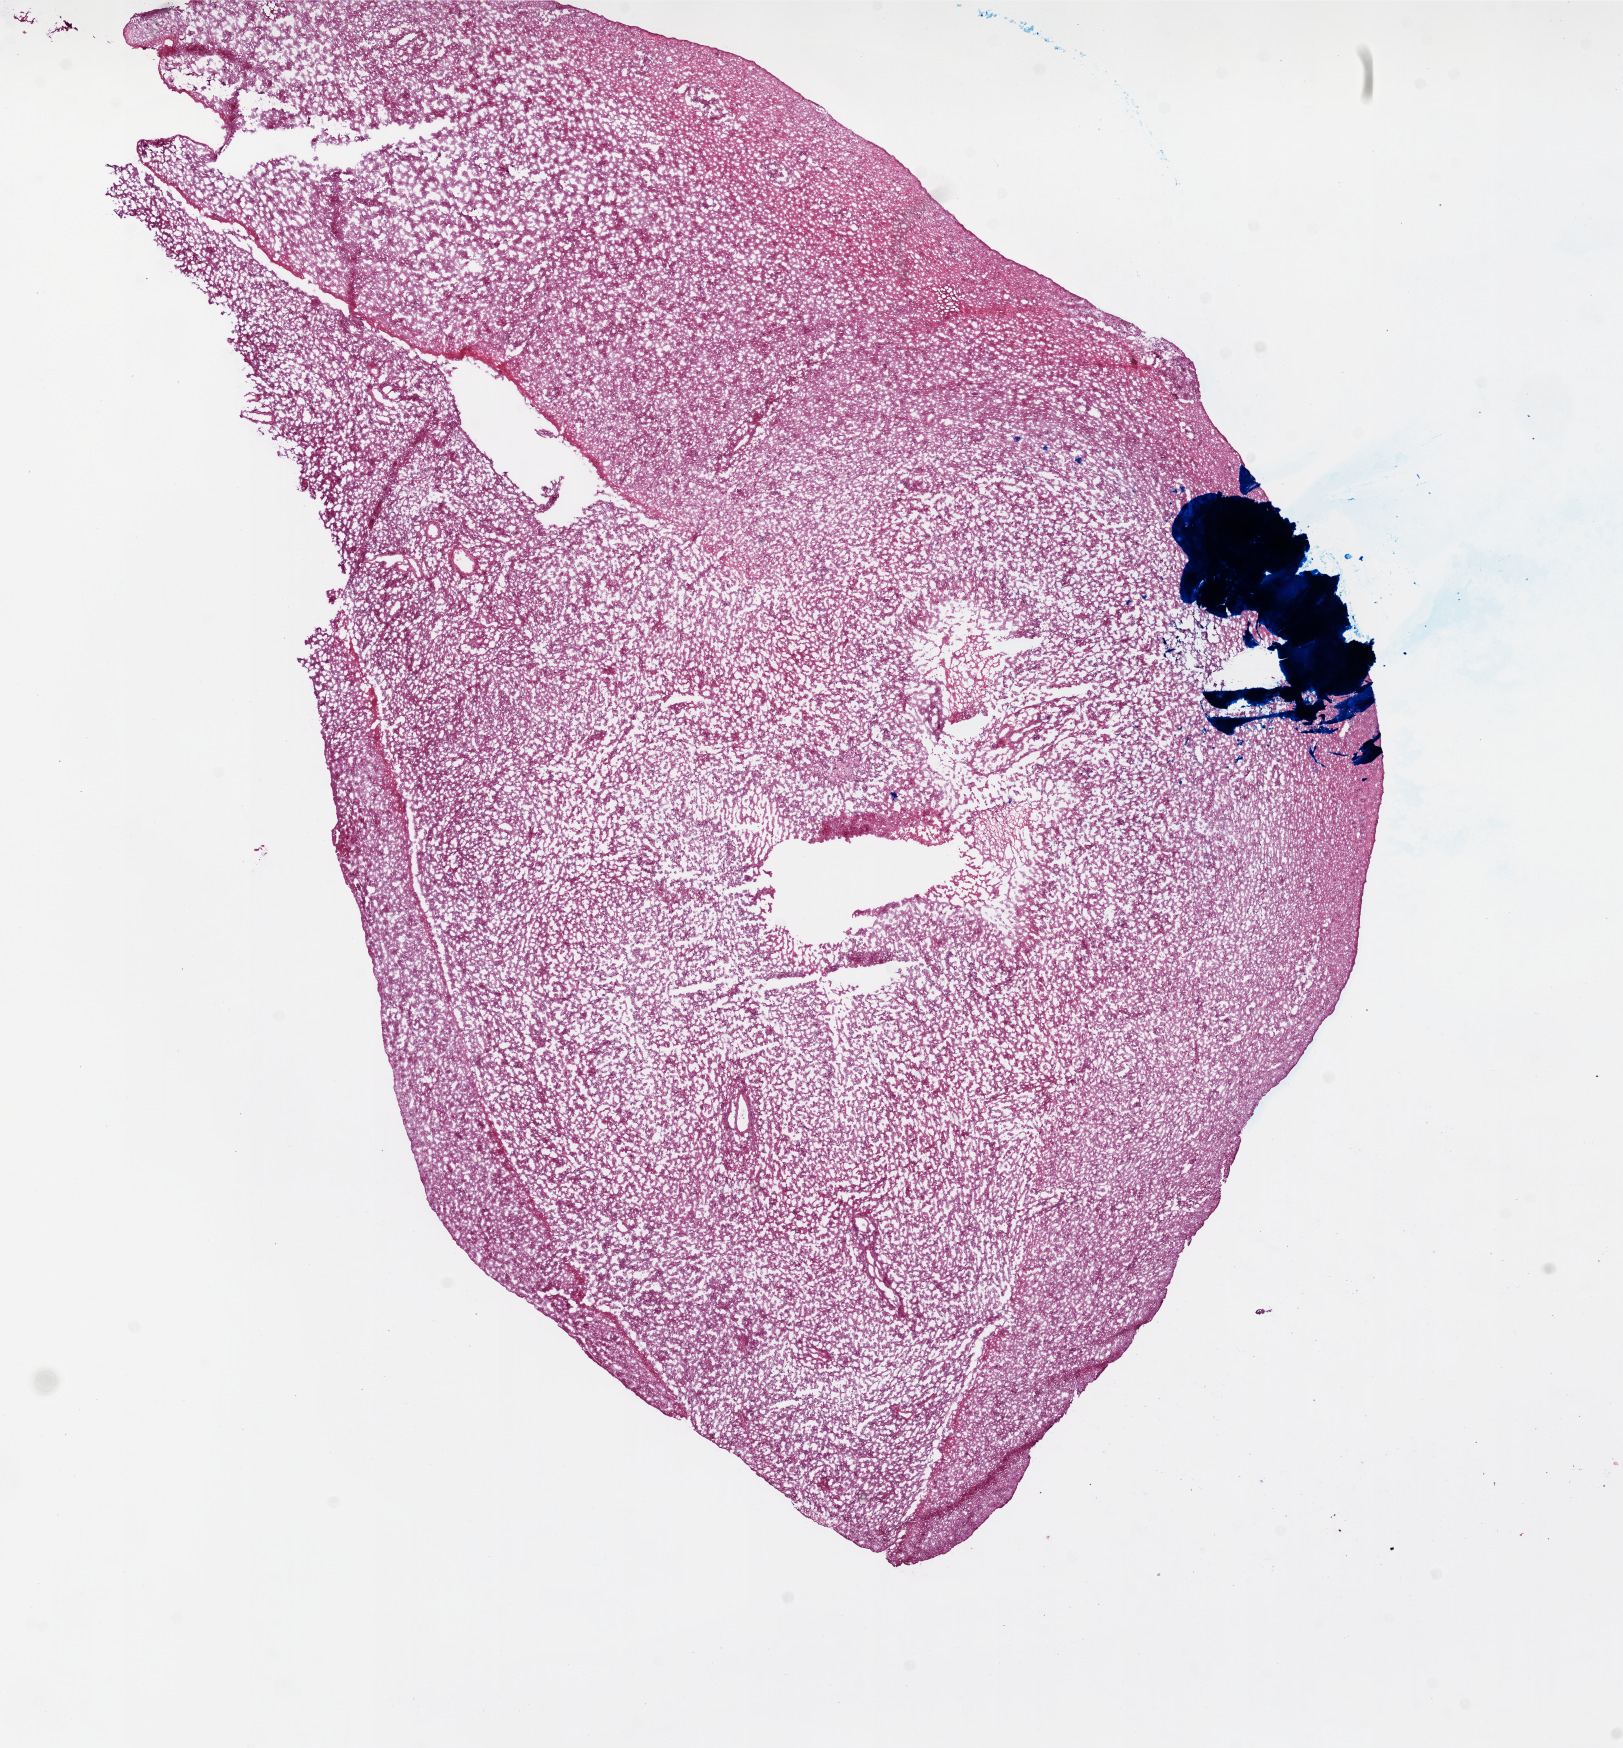
Digitized Hematoxylin and eosin (H&E) stained tissue section (whole slide), shown as a low-resolution overview of the whole scanned area (about 13.0 x 14.0 mm, from a 20x scan); frozen section; brain, primary tumour sample. Female patient; age at initial diagnosis 82 years. Slide review estimates, as recorded: tumour cells 50%, tumour nuclei 90%, normal cells 0%, stromal cells 35%, necrosis 15%. Infiltration values recorded for this section: lymphocyte infiltration 0%.
- diagnosis: Glioblastoma